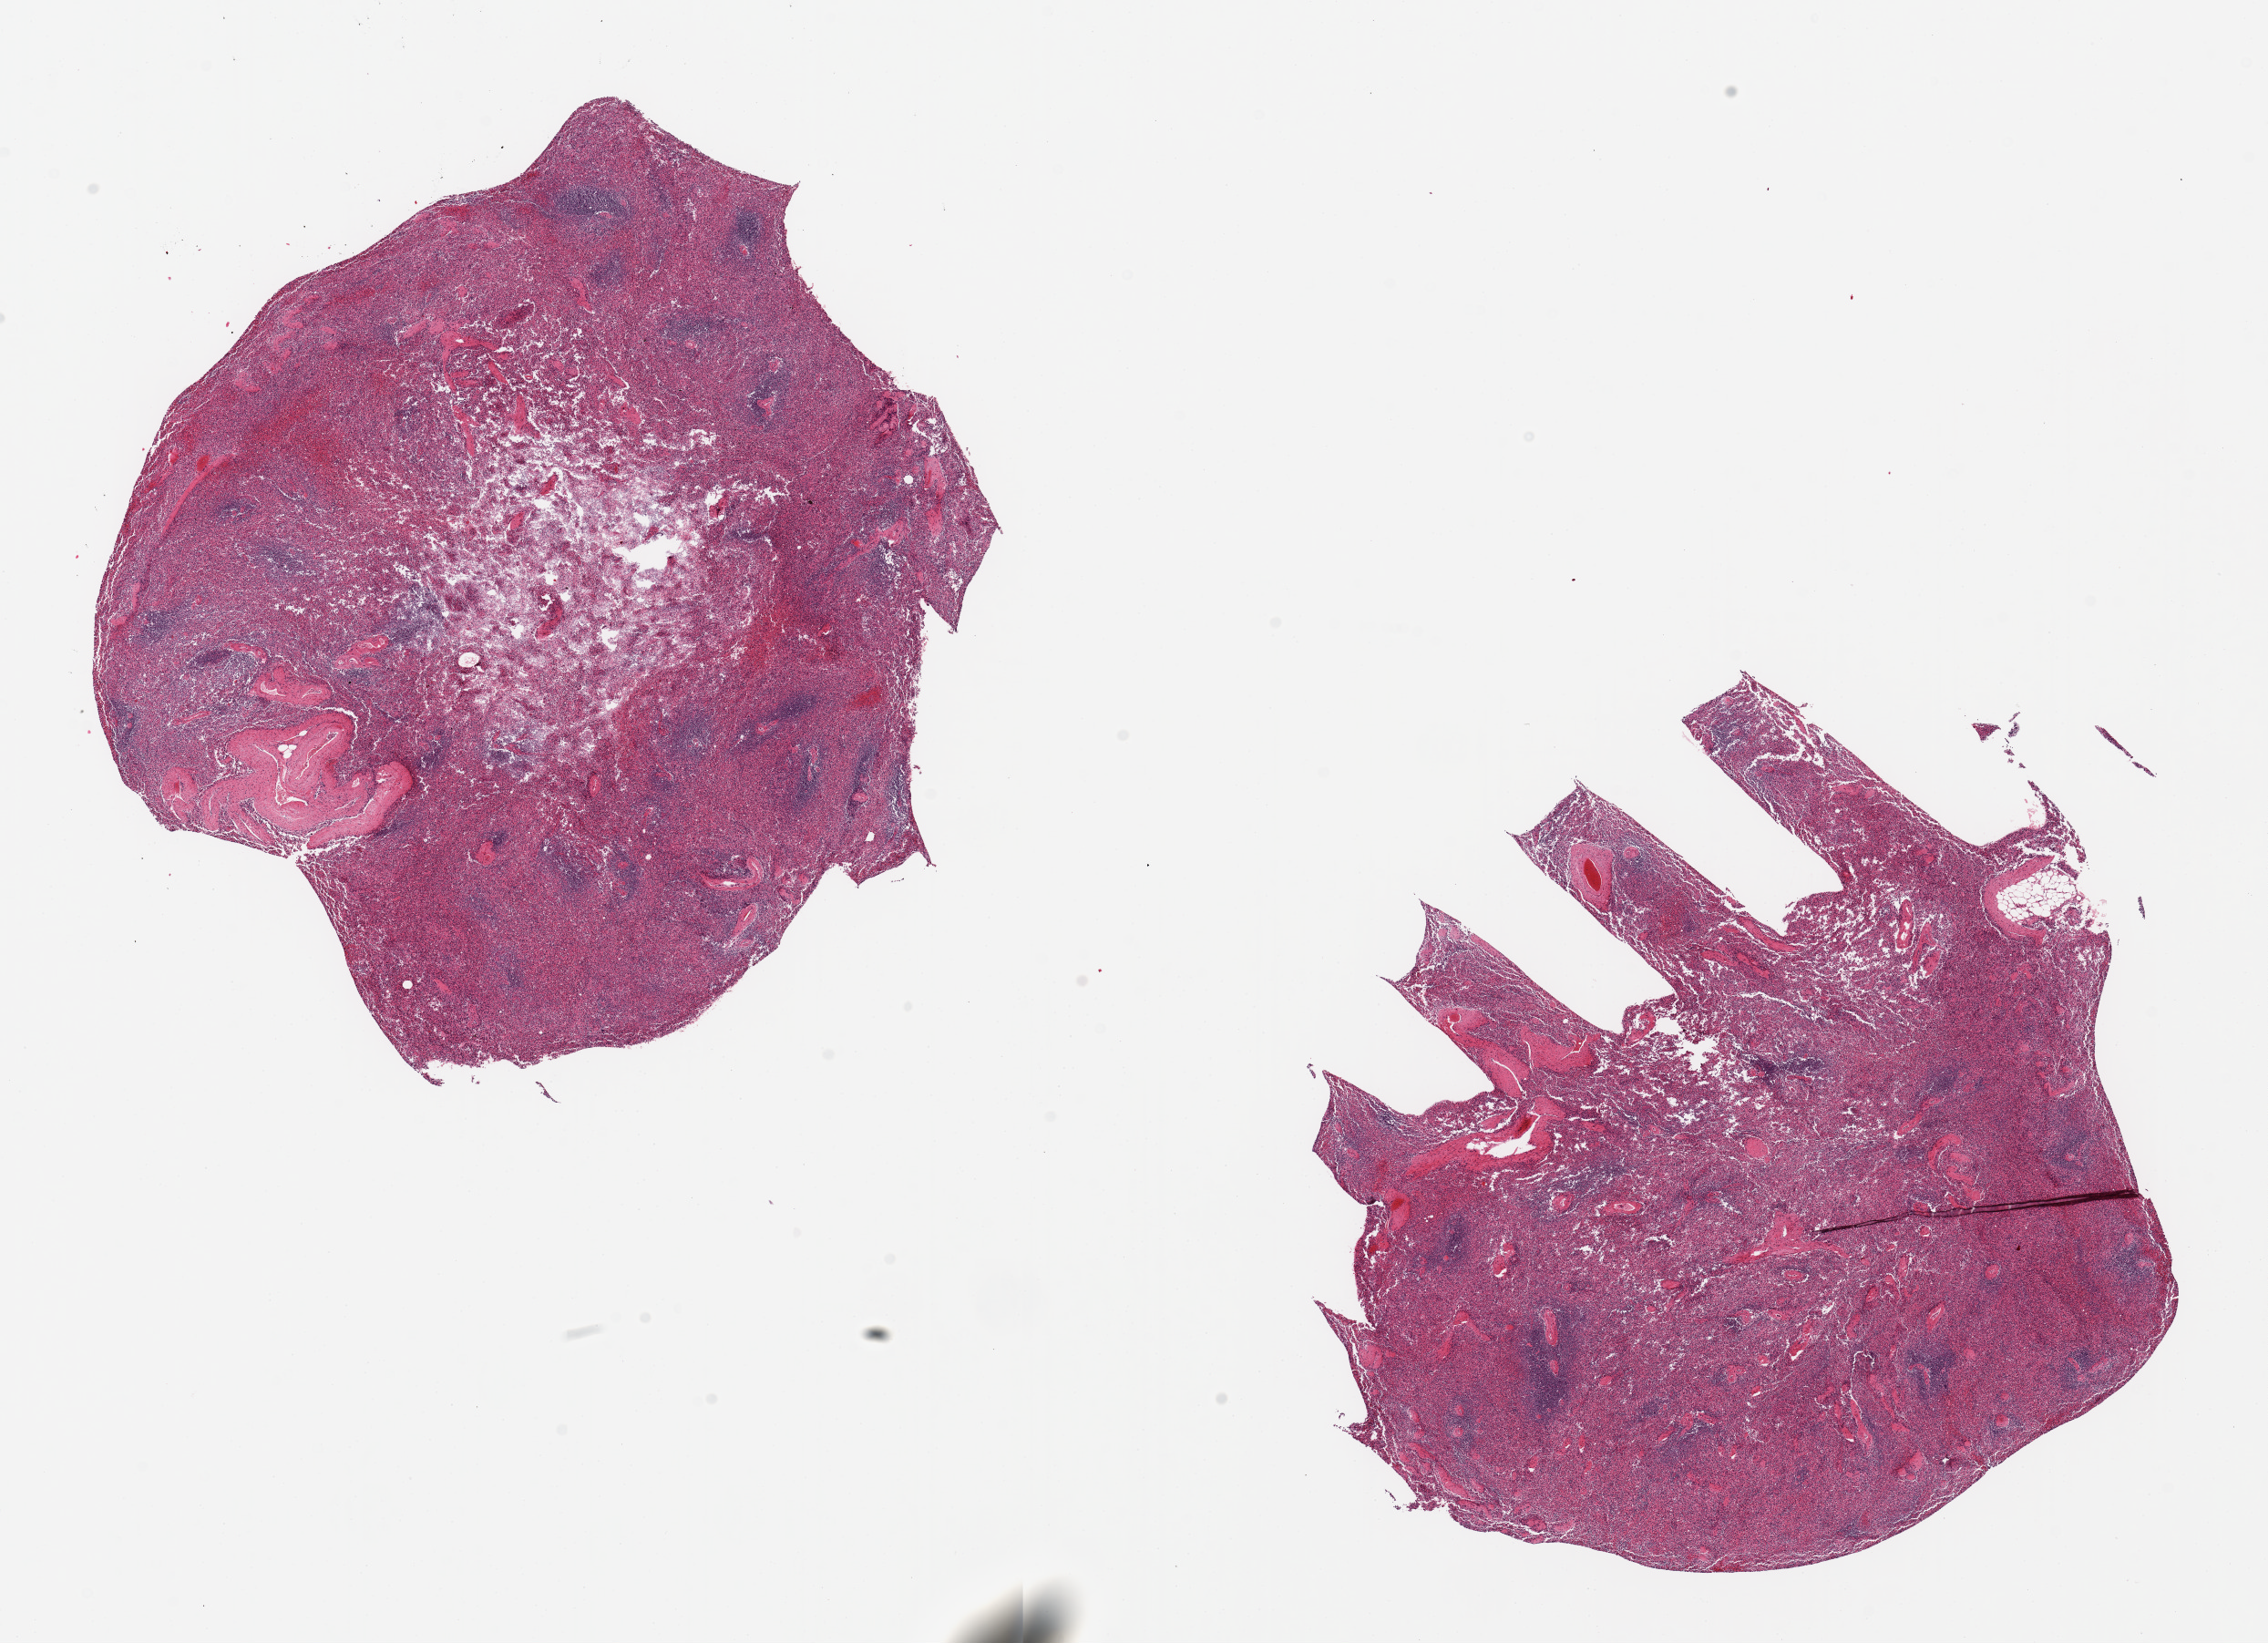
H&E whole-slide image, shown as a low-resolution overview of the whole scanned area (about 19.7 x 14.3 mm). PAXgene-fixed paraffin-embedded (PFPE) section. Section of spleen (target tissue). Donor tissue sample. Donor sex: female.
- pathologist's review note for this sample: 2 pieces, 8x7.5 & 9x7mm; autolysis varies from 2 to 3